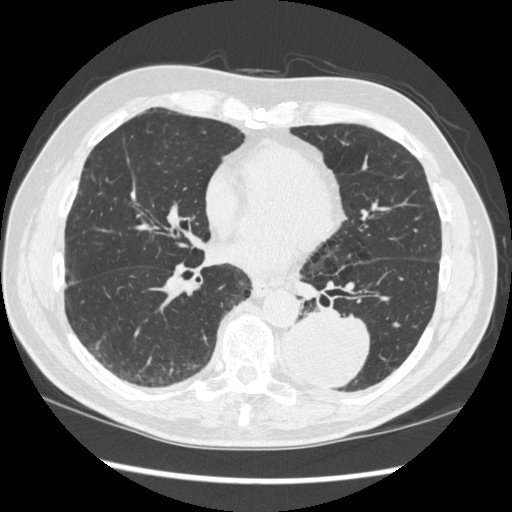
Low-dose screening chest CT, one axial slice; position 144 of 348 along the scan axis; reconstruction kernel STANDARD; lung window (W 1500 / L -600 HU); 1.25 mm slice thickness; 512 × 512 image matrix, field of view 360 × 360 mm.
Annotated regions visible in this slice (manually delineated by an expert):
- lesion 1 (tumor, lower lobe of left lung): bounding box (x1, y1, x2, y2) in pixels: (283, 311, 370, 390)